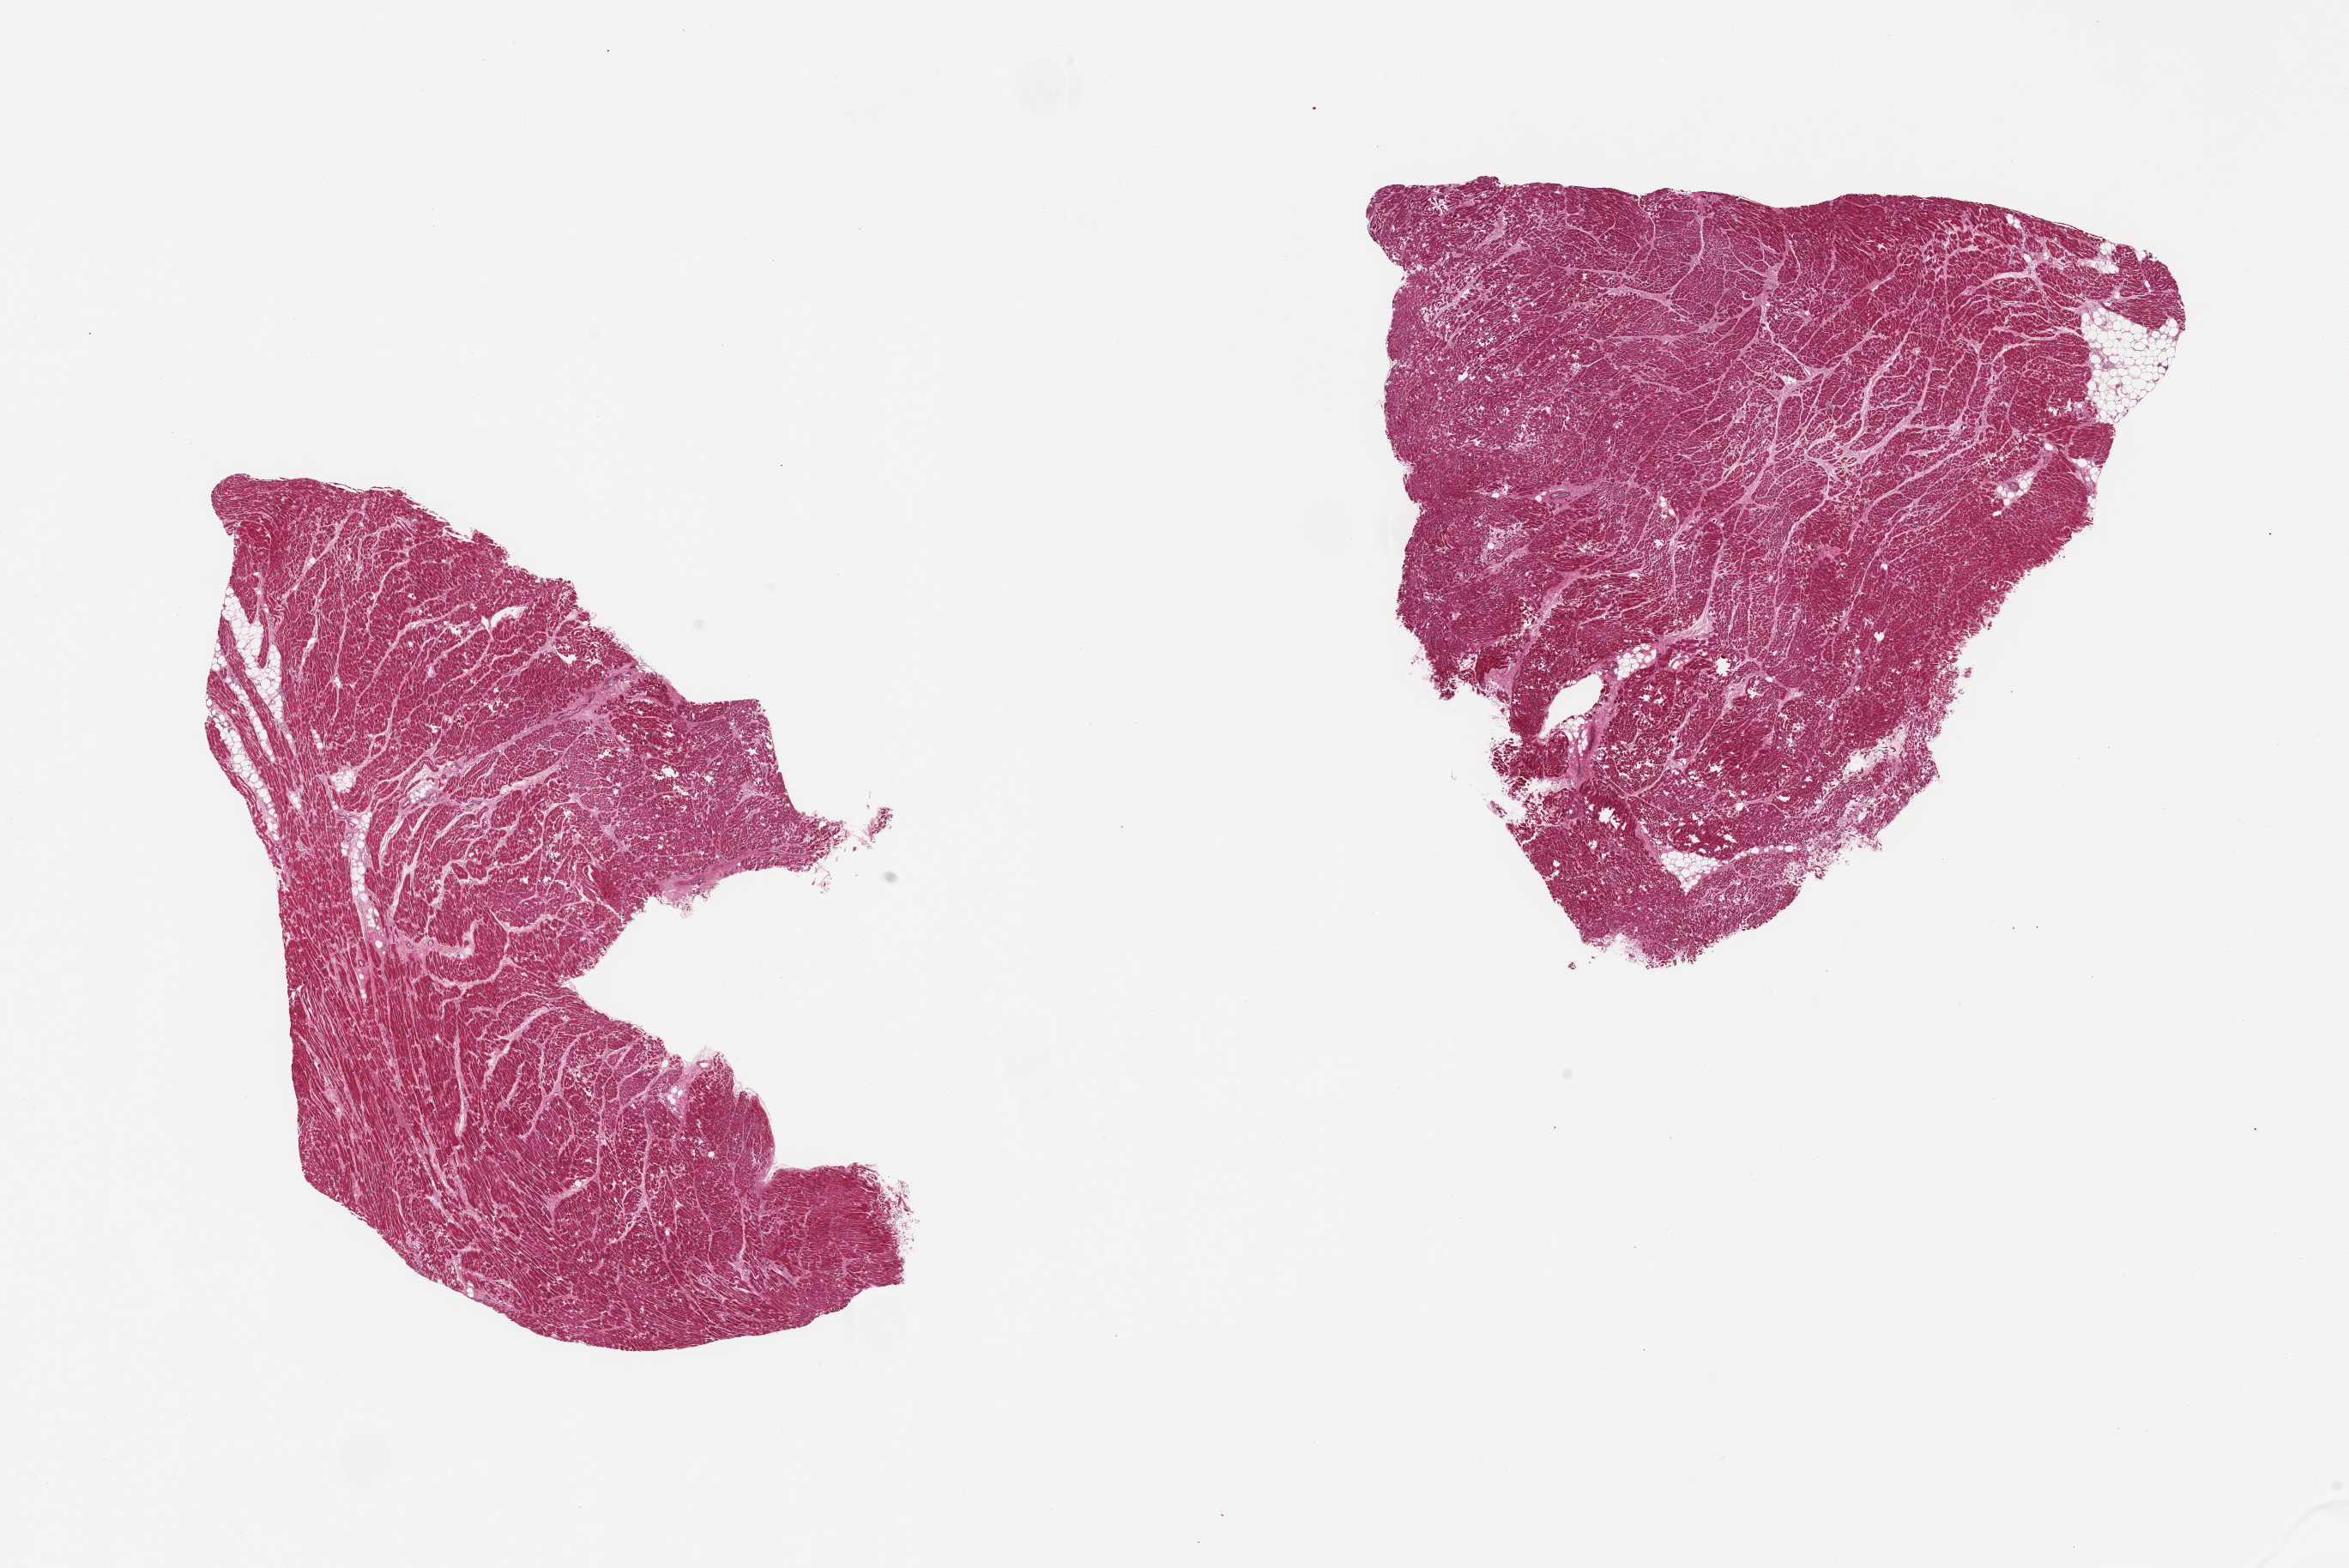
Whole-slide image, hematoxylin and eosin (H&E) stain, brightfield, low-resolution overview of the scanned area, about 21.7 x 14.5 mm; PAXgene-fixed, paraffin-embedded tissue; target tissue: heart; donor tissue sample. Male donor.
* reviewer comment on this tissue sample: 2 pieces, moderate interstitial fibrosis/chronic ischemic changes